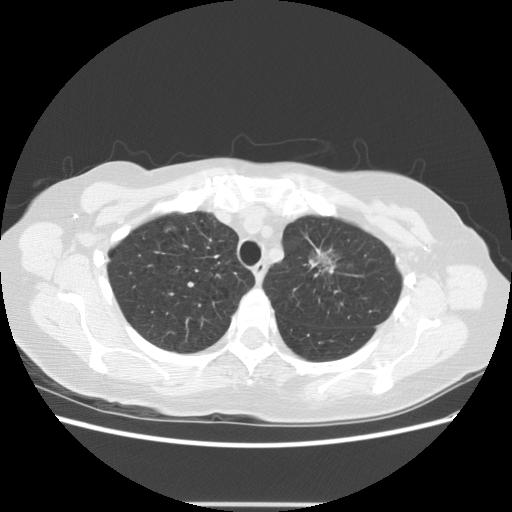
Low-dose screening chest CT, one axial slice. Position 100 of 126 along the scan axis. Reconstruction kernel STANDARD. Lung window (W 1500 / L -600 HU). 2.5 mm slice thickness. 512 × 512 image matrix, field of view 360 × 360 mm.
Annotated regions visible in this slice (outlined manually by an expert reader):
- lesion 2 (tumor, upper lobe of left lung): box from (x=312, y=251) to (x=334, y=272) px